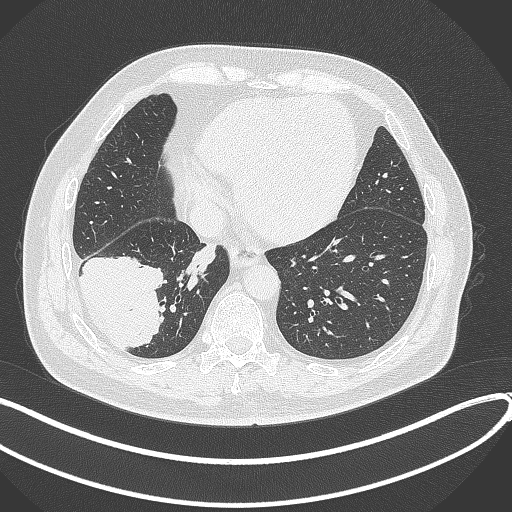
Chest CT, one axial slice. Slice 106 of 360 in the series (ordered by position). Reconstruction kernel B70f. Lung window (W 1500 / L -600 HU). 1 mm slice thickness. 512 × 512 image matrix, field of view 400 × 400 mm. Patient: male, 59 years.
Structures marked on this image (rectangle marked by the reading radiologist):
- lung tumour (recorded histology: adenocarcinoma): bounding box (x1, y1, x2, y2) in pixels: (74, 251, 170, 353)